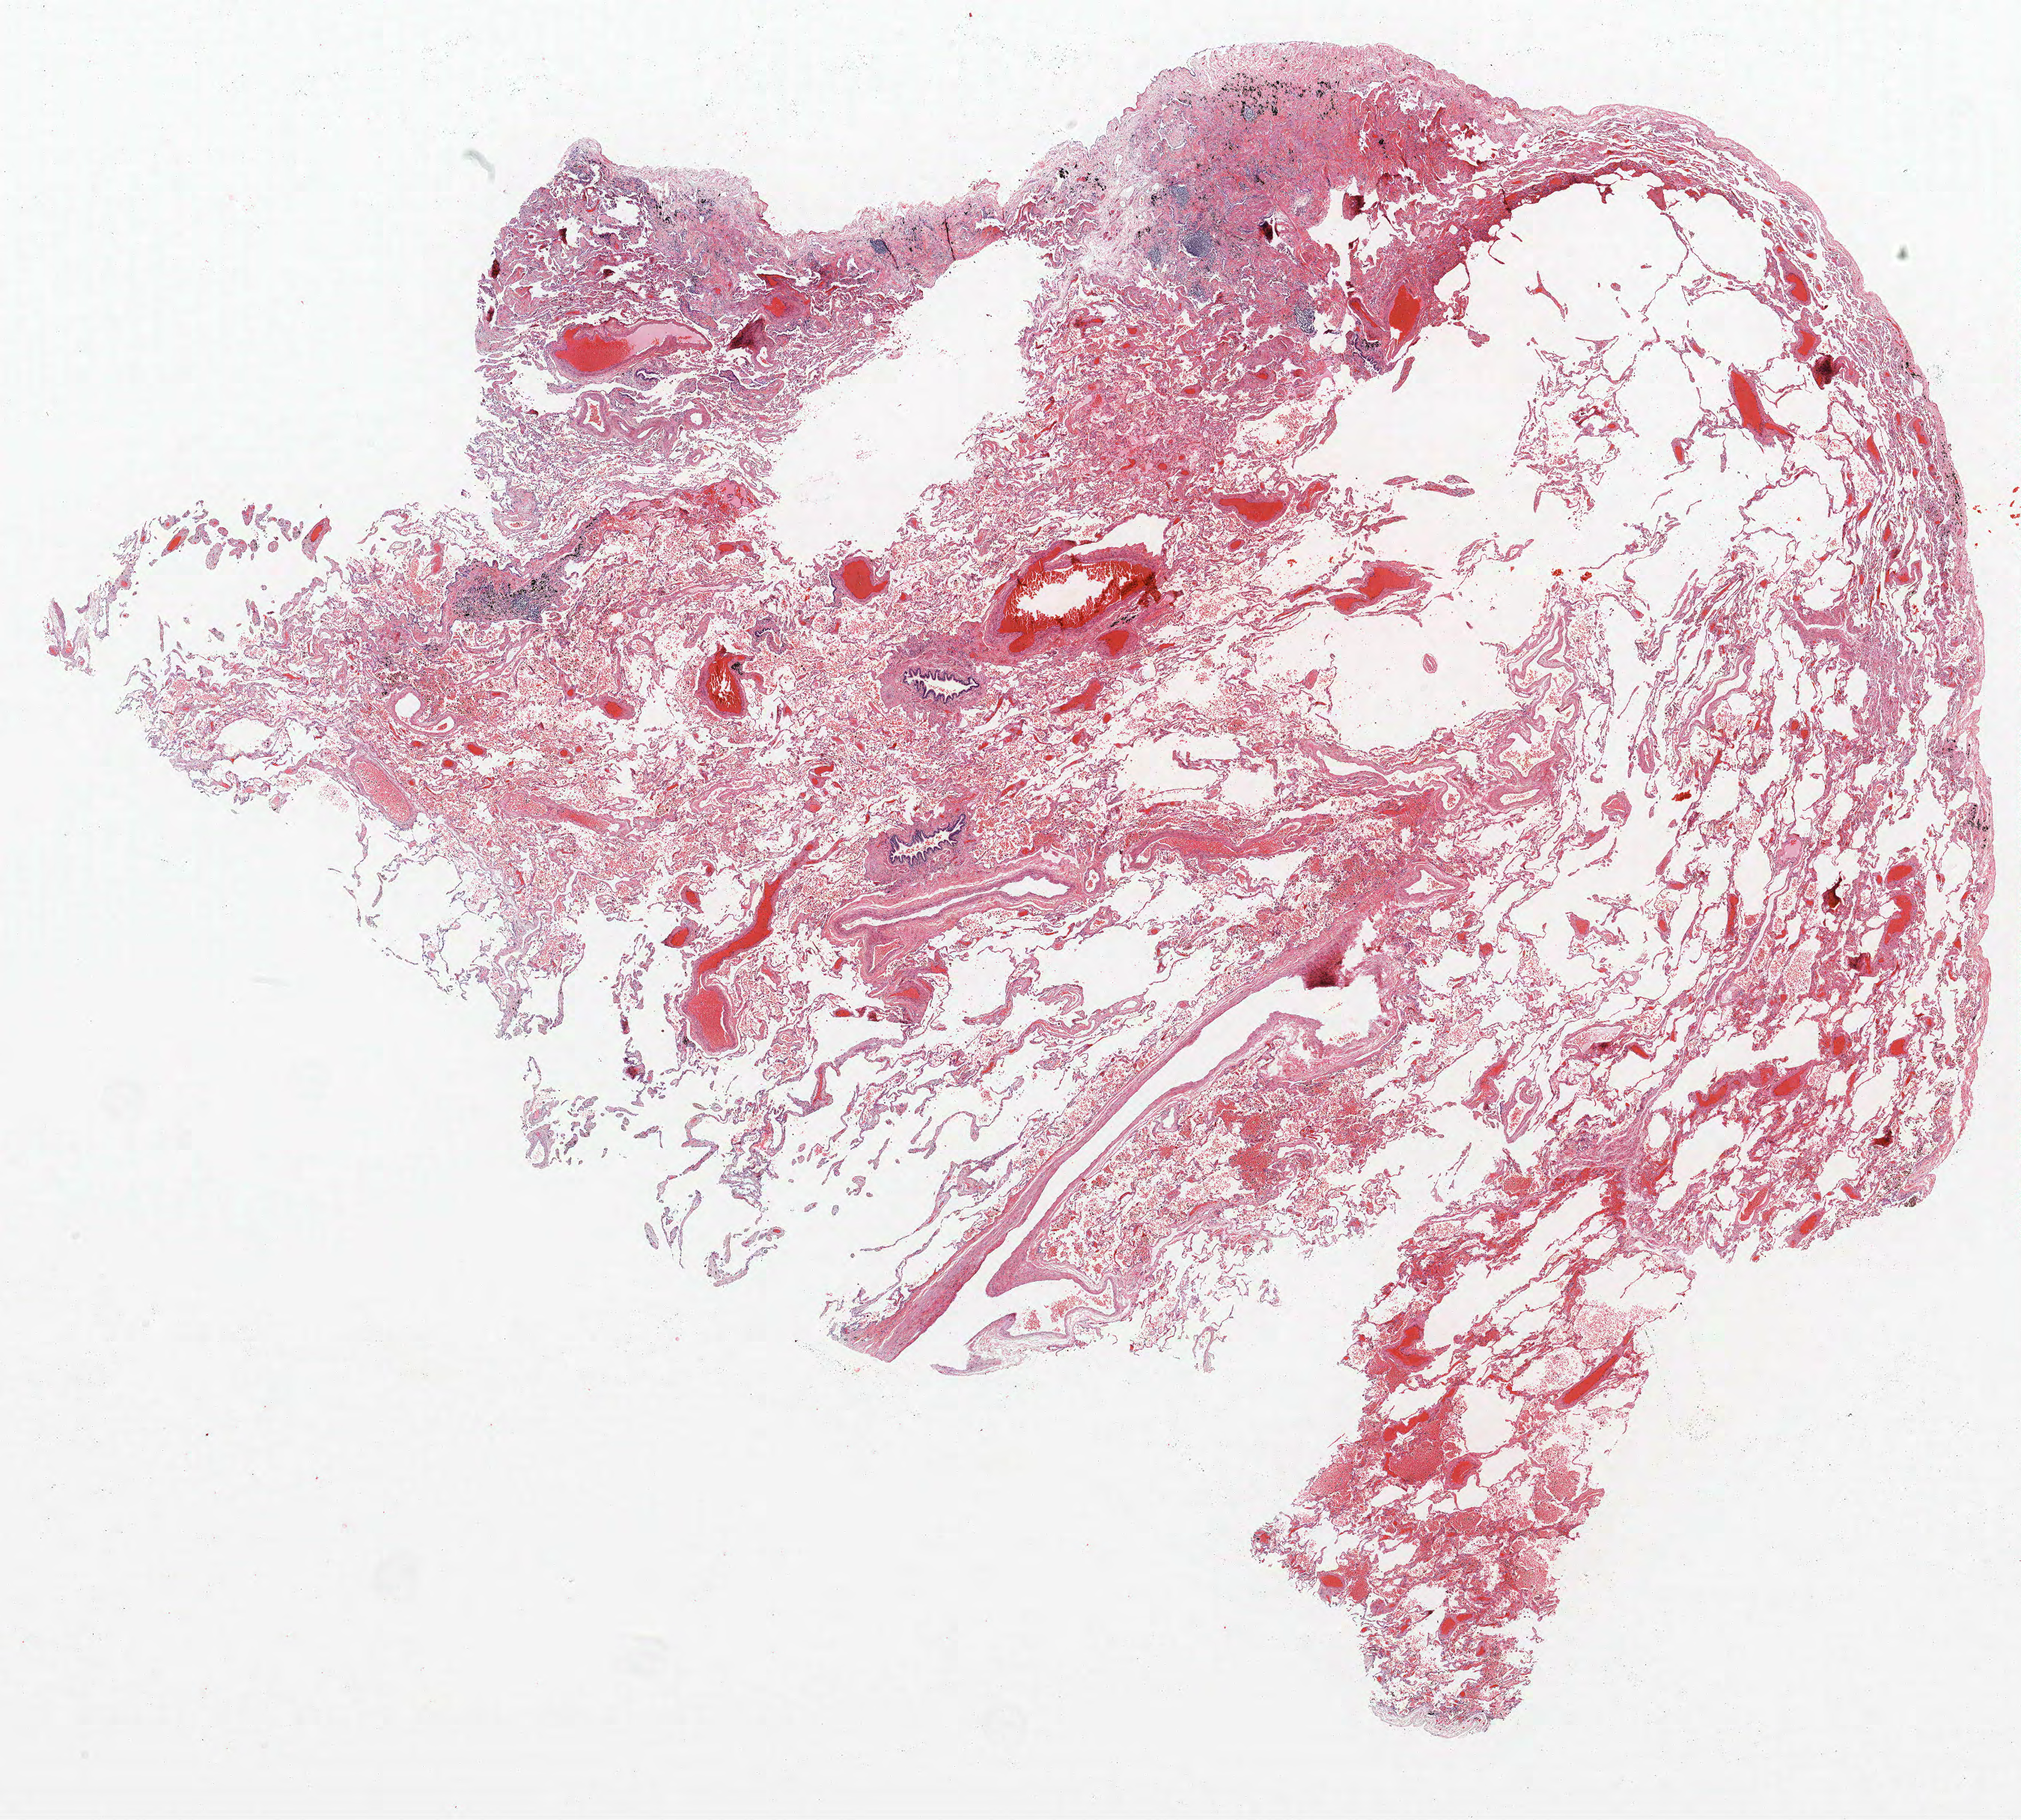
Whole-slide histology image, H&E-stained, shown as a low-resolution overview of the whole scanned area (about 21.6 x 19.5 mm, from a 40x scan), formalin-fixed paraffin-embedded (FFPE) section, lung tissue. Male patient, aged 70 at enrolment. Current smoker at enrolment.
Participant's lung-cancer diagnosis: Small cell carcinoma, NOS. Primary tumour location (clinical record): right upper lobe. Stage (AJCC 6th edition): IA. Tumour size (pathology): 11 mm.